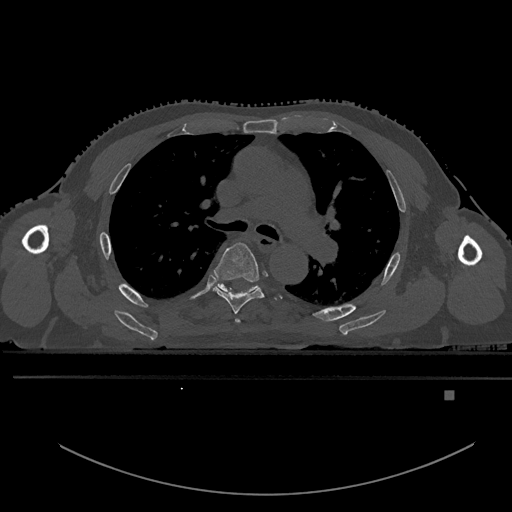
CT including the spine, one axial slice. Position 352 of 969 along the scan axis. Bone window (W 1800 / L 400 HU). 0.5 mm slice thickness. 512 × 512 image matrix, field of view 456 × 456 mm. Patient: male, 82 years. Case-level facts recorded for this patient, not image findings: primary cancer: prostate.
Outlined on this slice (semi-automatically segmented with operator editing):
- T4 vertebra: box from (x=235, y=319) to (x=240, y=324) px
- T5 vertebra: (x=213, y=242)–(x=276, y=314)
- T6 vertebra: (x=212, y=284)–(x=258, y=293)